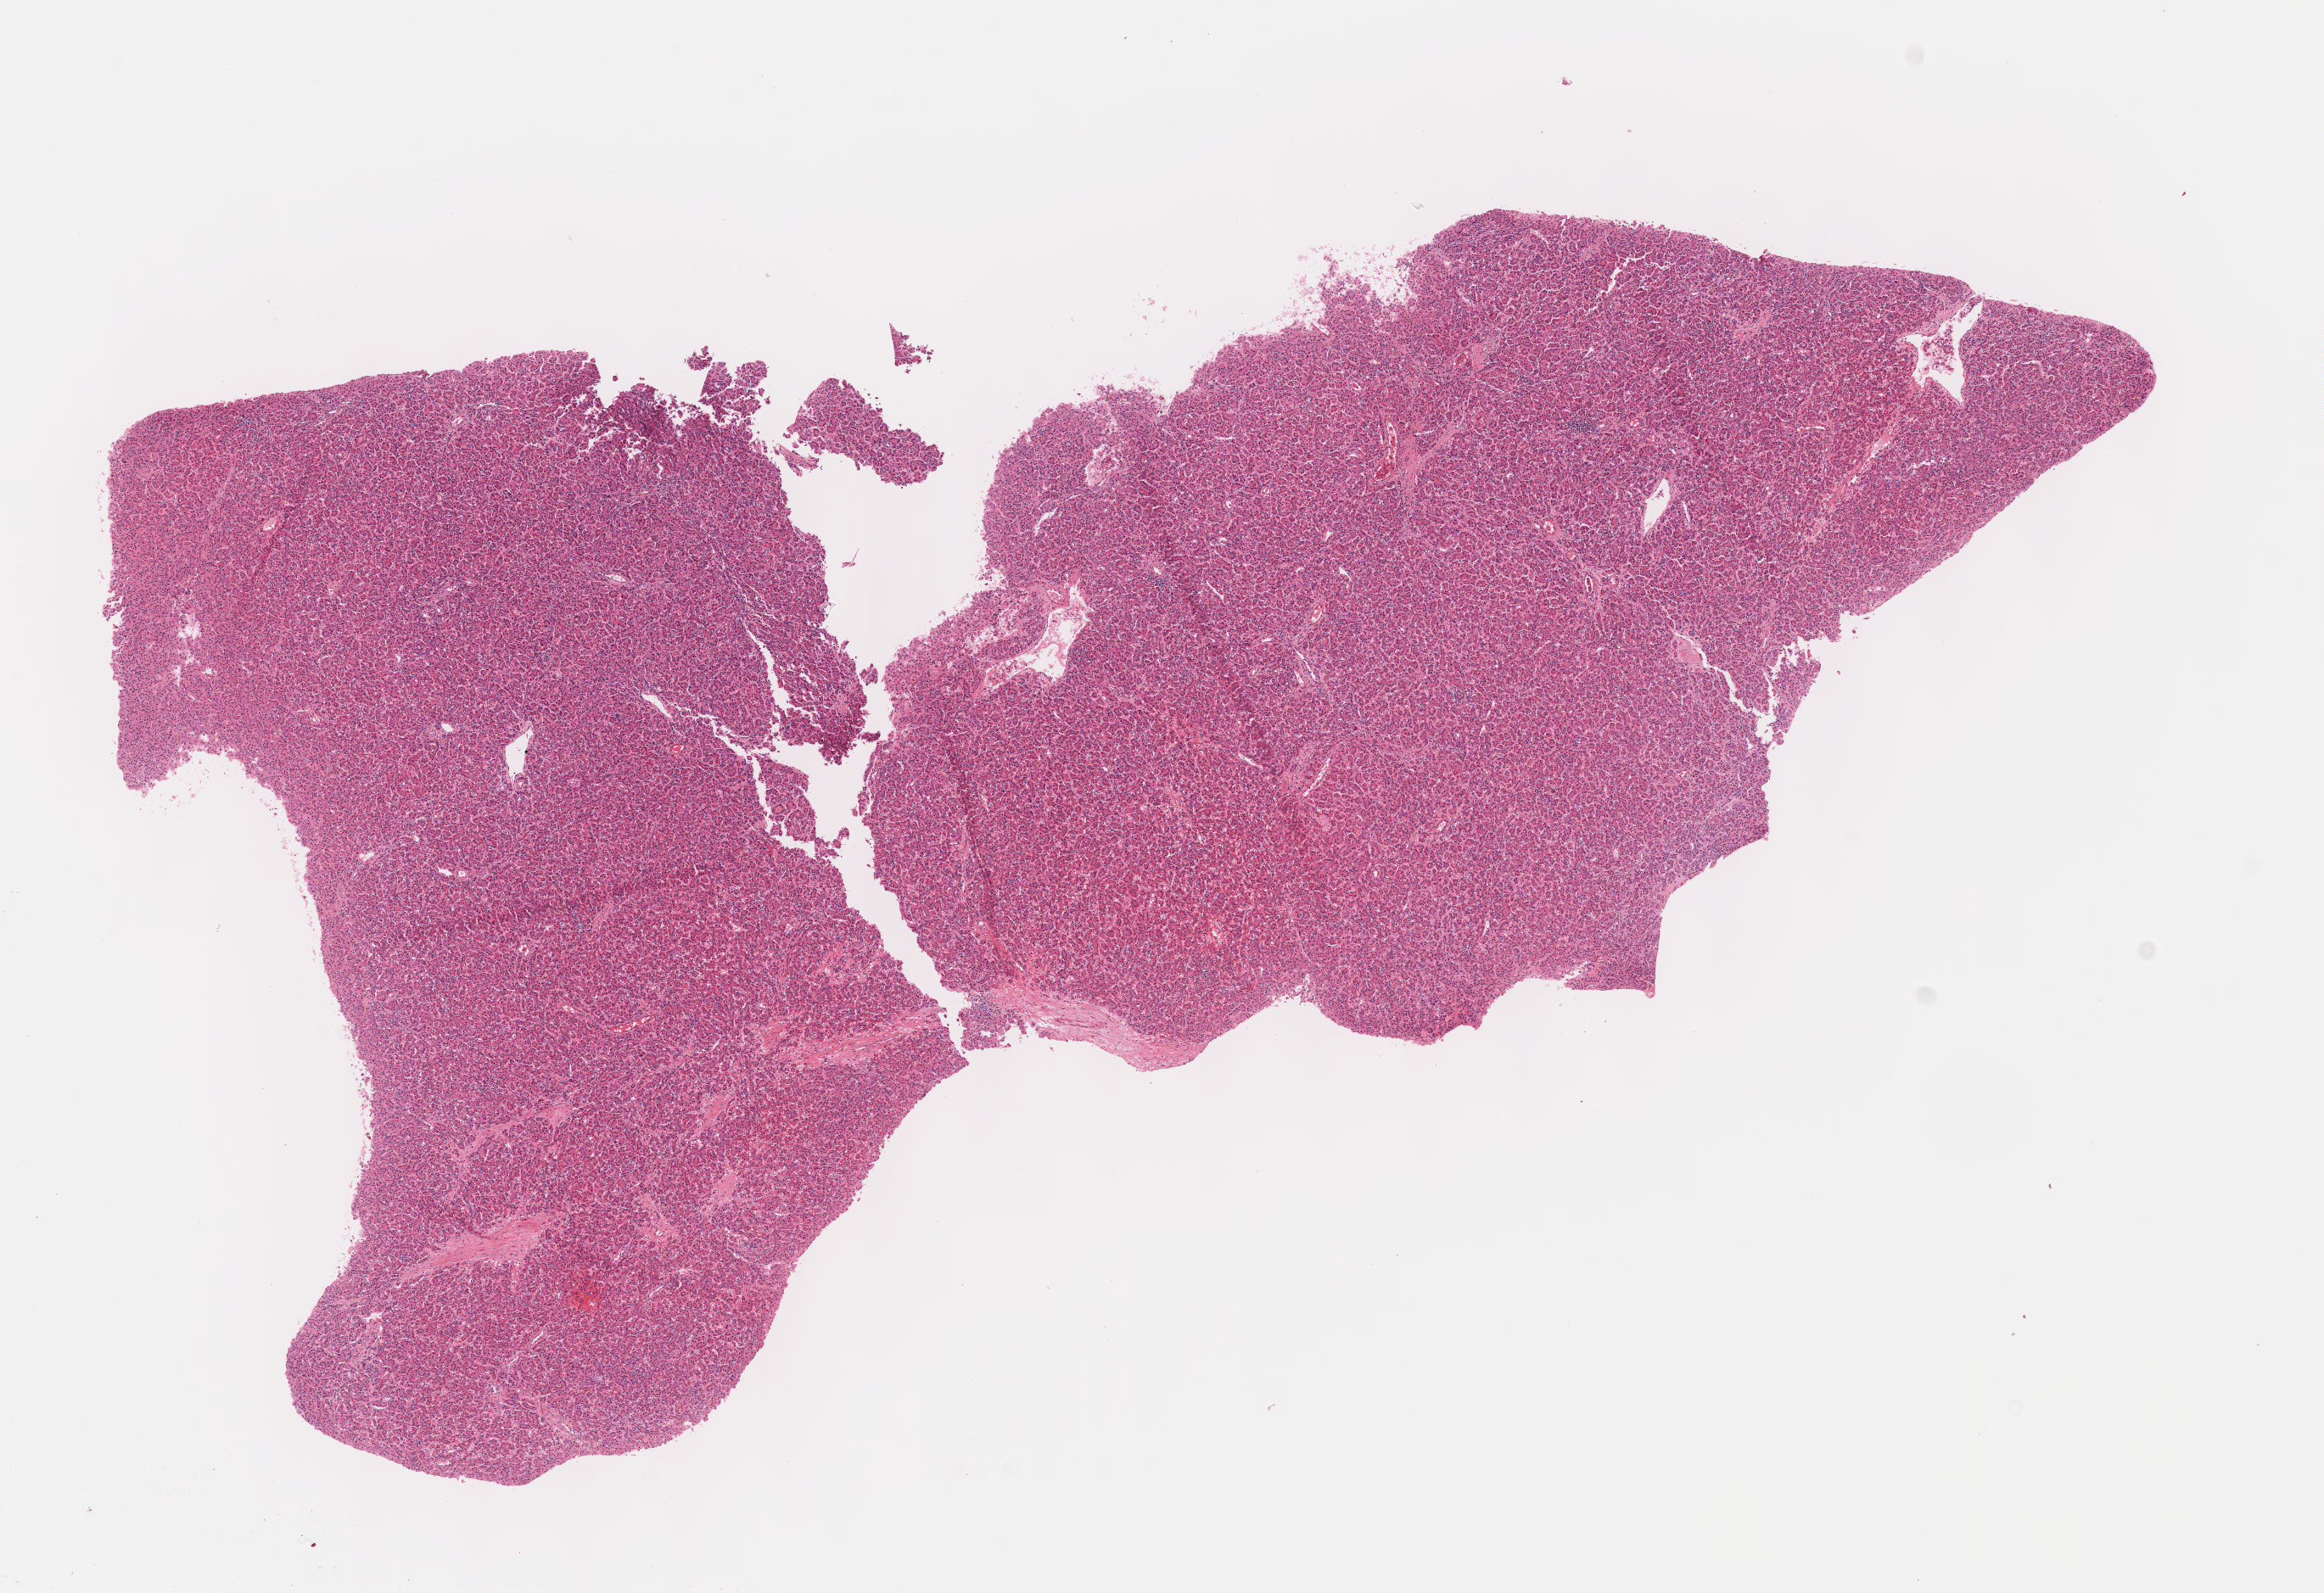
Digitized H&E-stained tissue section (whole slide) — whole scanned area (about 11.1 x 7.6 mm, from a 40x scan) shown as a low-resolution overview; FFPE section; sample: primary tumour, liver. Male patient; age at initial diagnosis 73 years. Histologic grade: G2 (moderately differentiated).
* AJCC pathologic stage: I (7th edition)
* pathologic diagnosis: Hepatocellular carcinoma, NOS